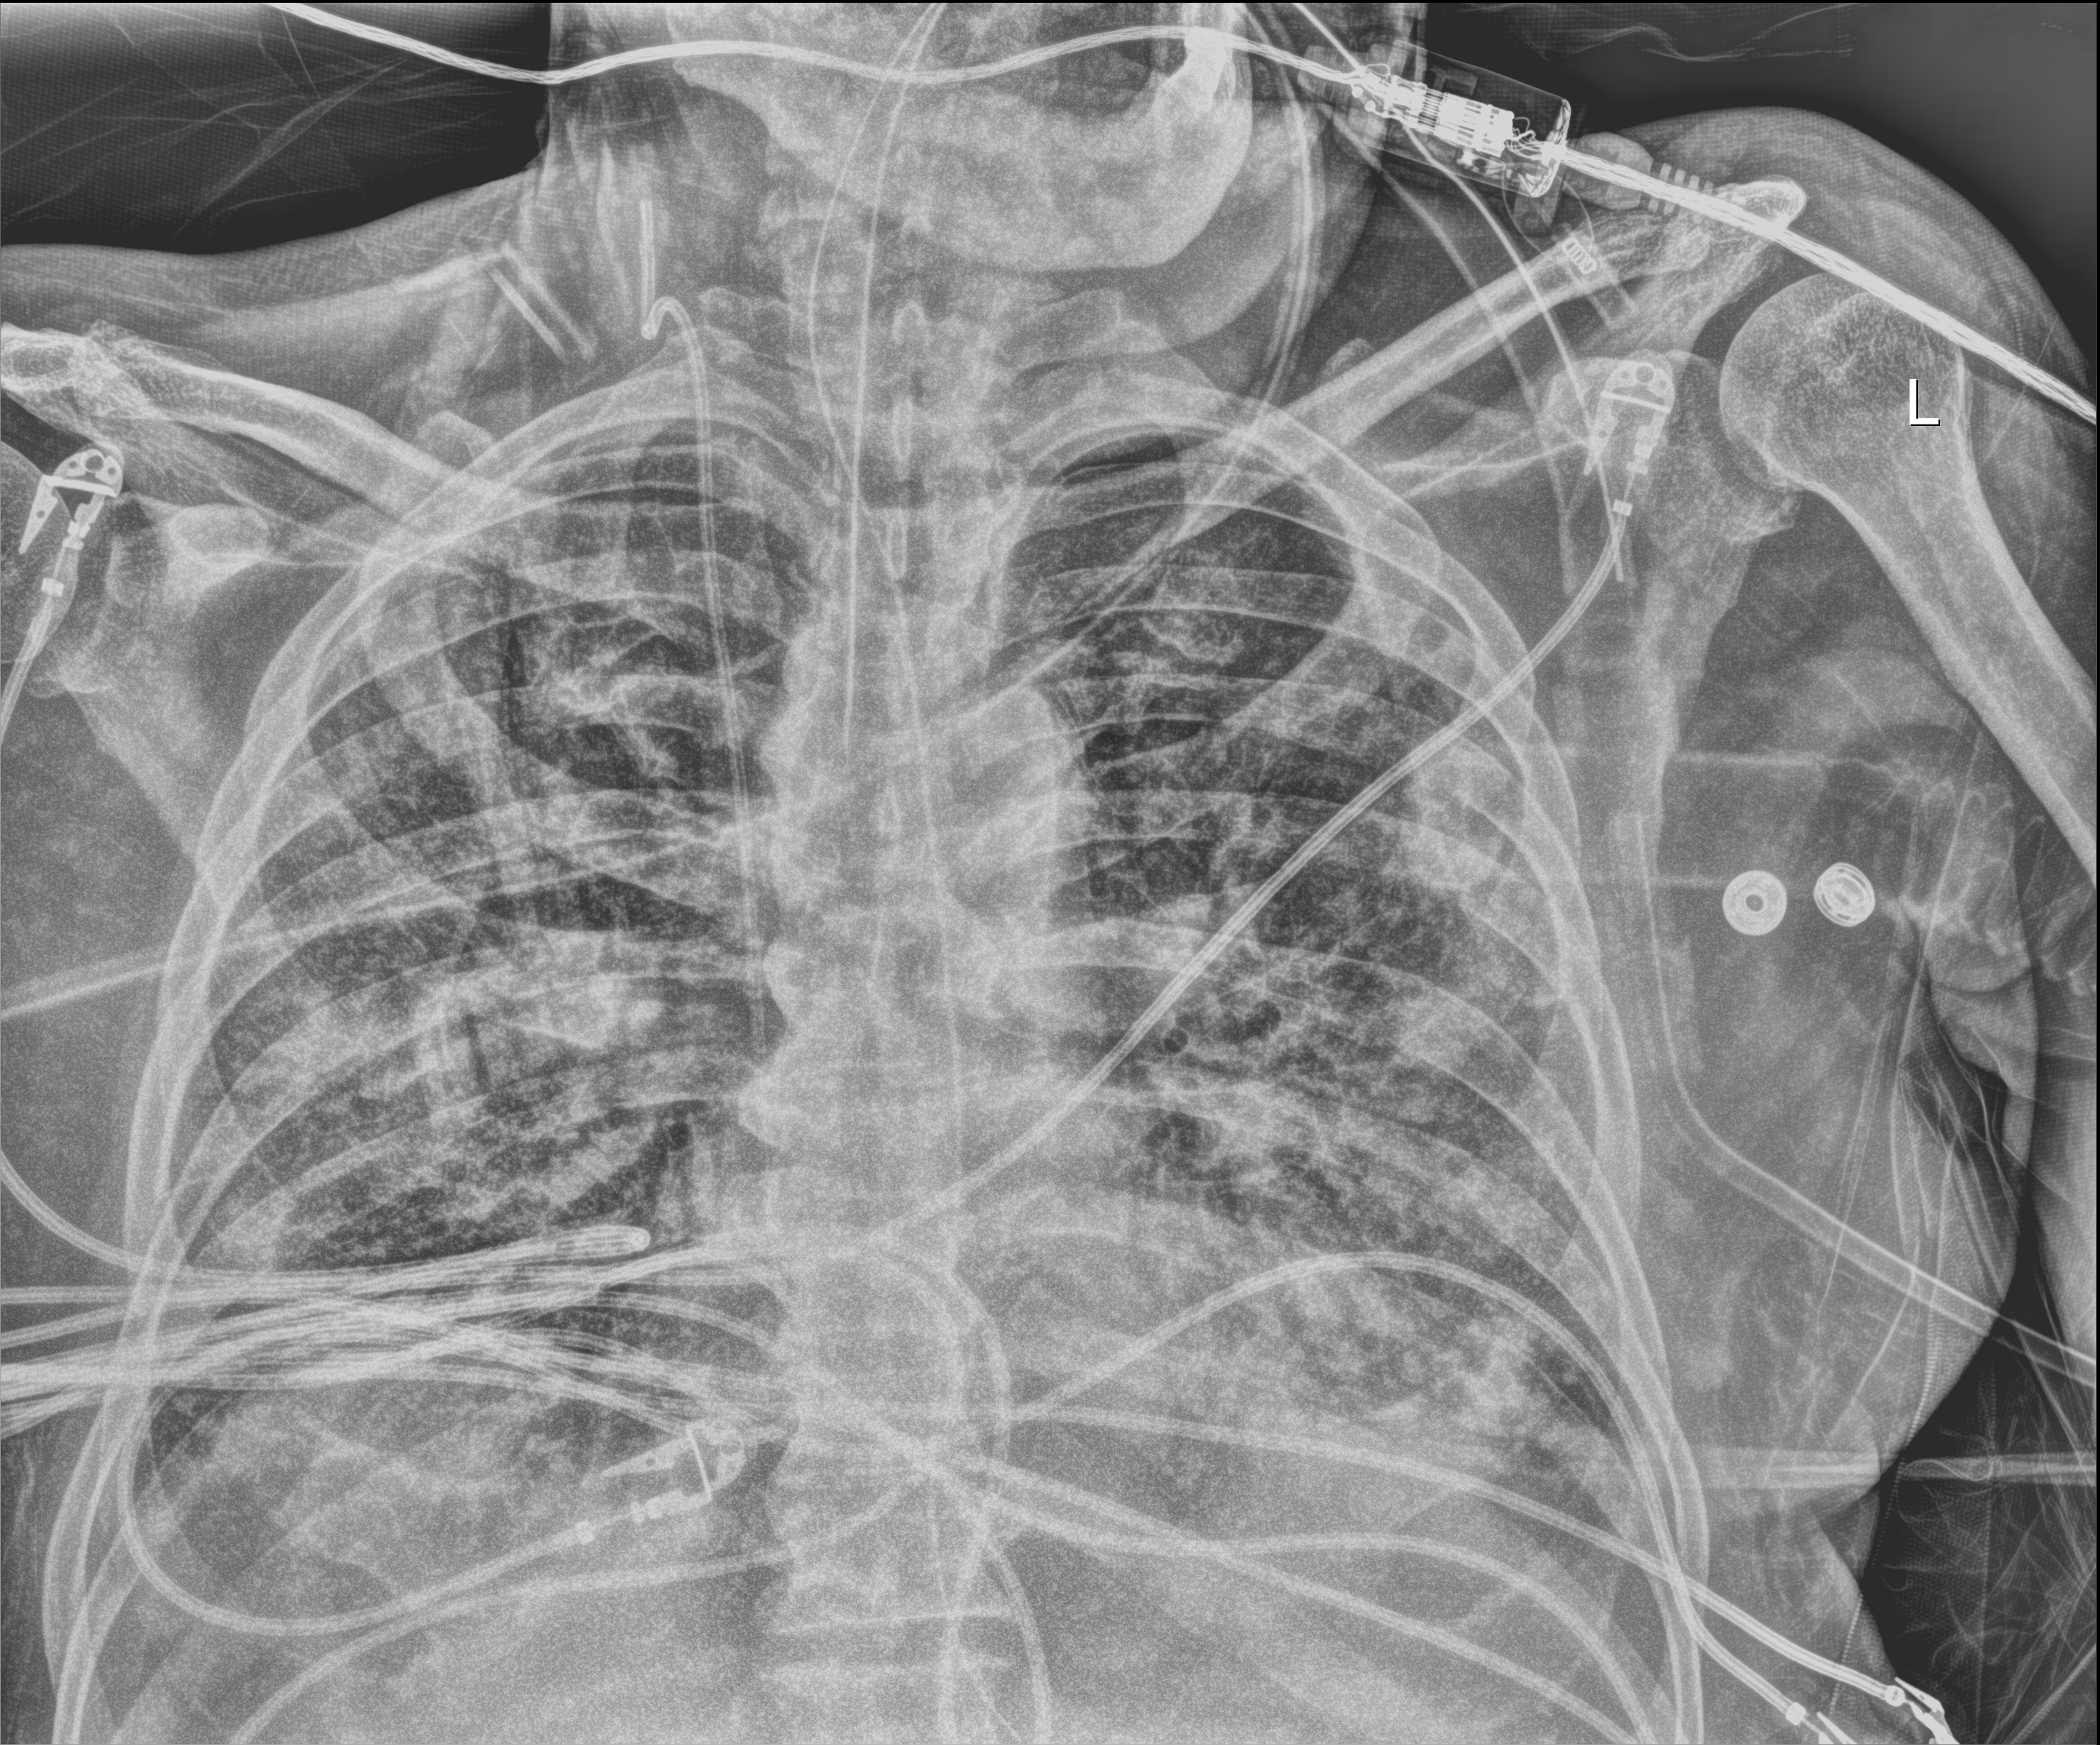
Bedside chest radiograph (digital radiography), anteroposterior (AP) projection. Patient hospitalised with COVID-19; male, aged 75–90 years.
Hospital-stay facts (about this admission, not read from this image; timing relative to this image not recorded): mechanically ventilated during this hospital stay: yes.